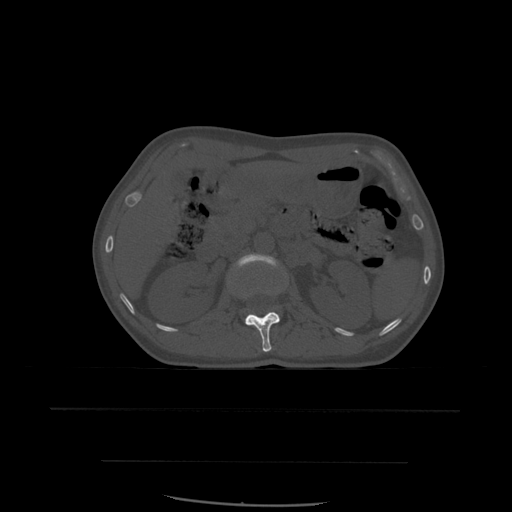
CT including the spine, one axial slice. Slice 241 of 574 in the series (ordered by position). Bone window (W 1800 / L 400 HU). 1.25 mm slice thickness. 512 × 512 image matrix, field of view 392 × 392 mm. Patient age 48 years. From the clinical record (not read from this slice): primary cancer: lung.
Annotated regions visible in this slice (semi-automatically segmented with operator editing):
- L1 vertebra: bounding box [x1, y1, x2, y2] px = [245, 312, 280, 352]
- L2 vertebra: [236, 254, 280, 268]